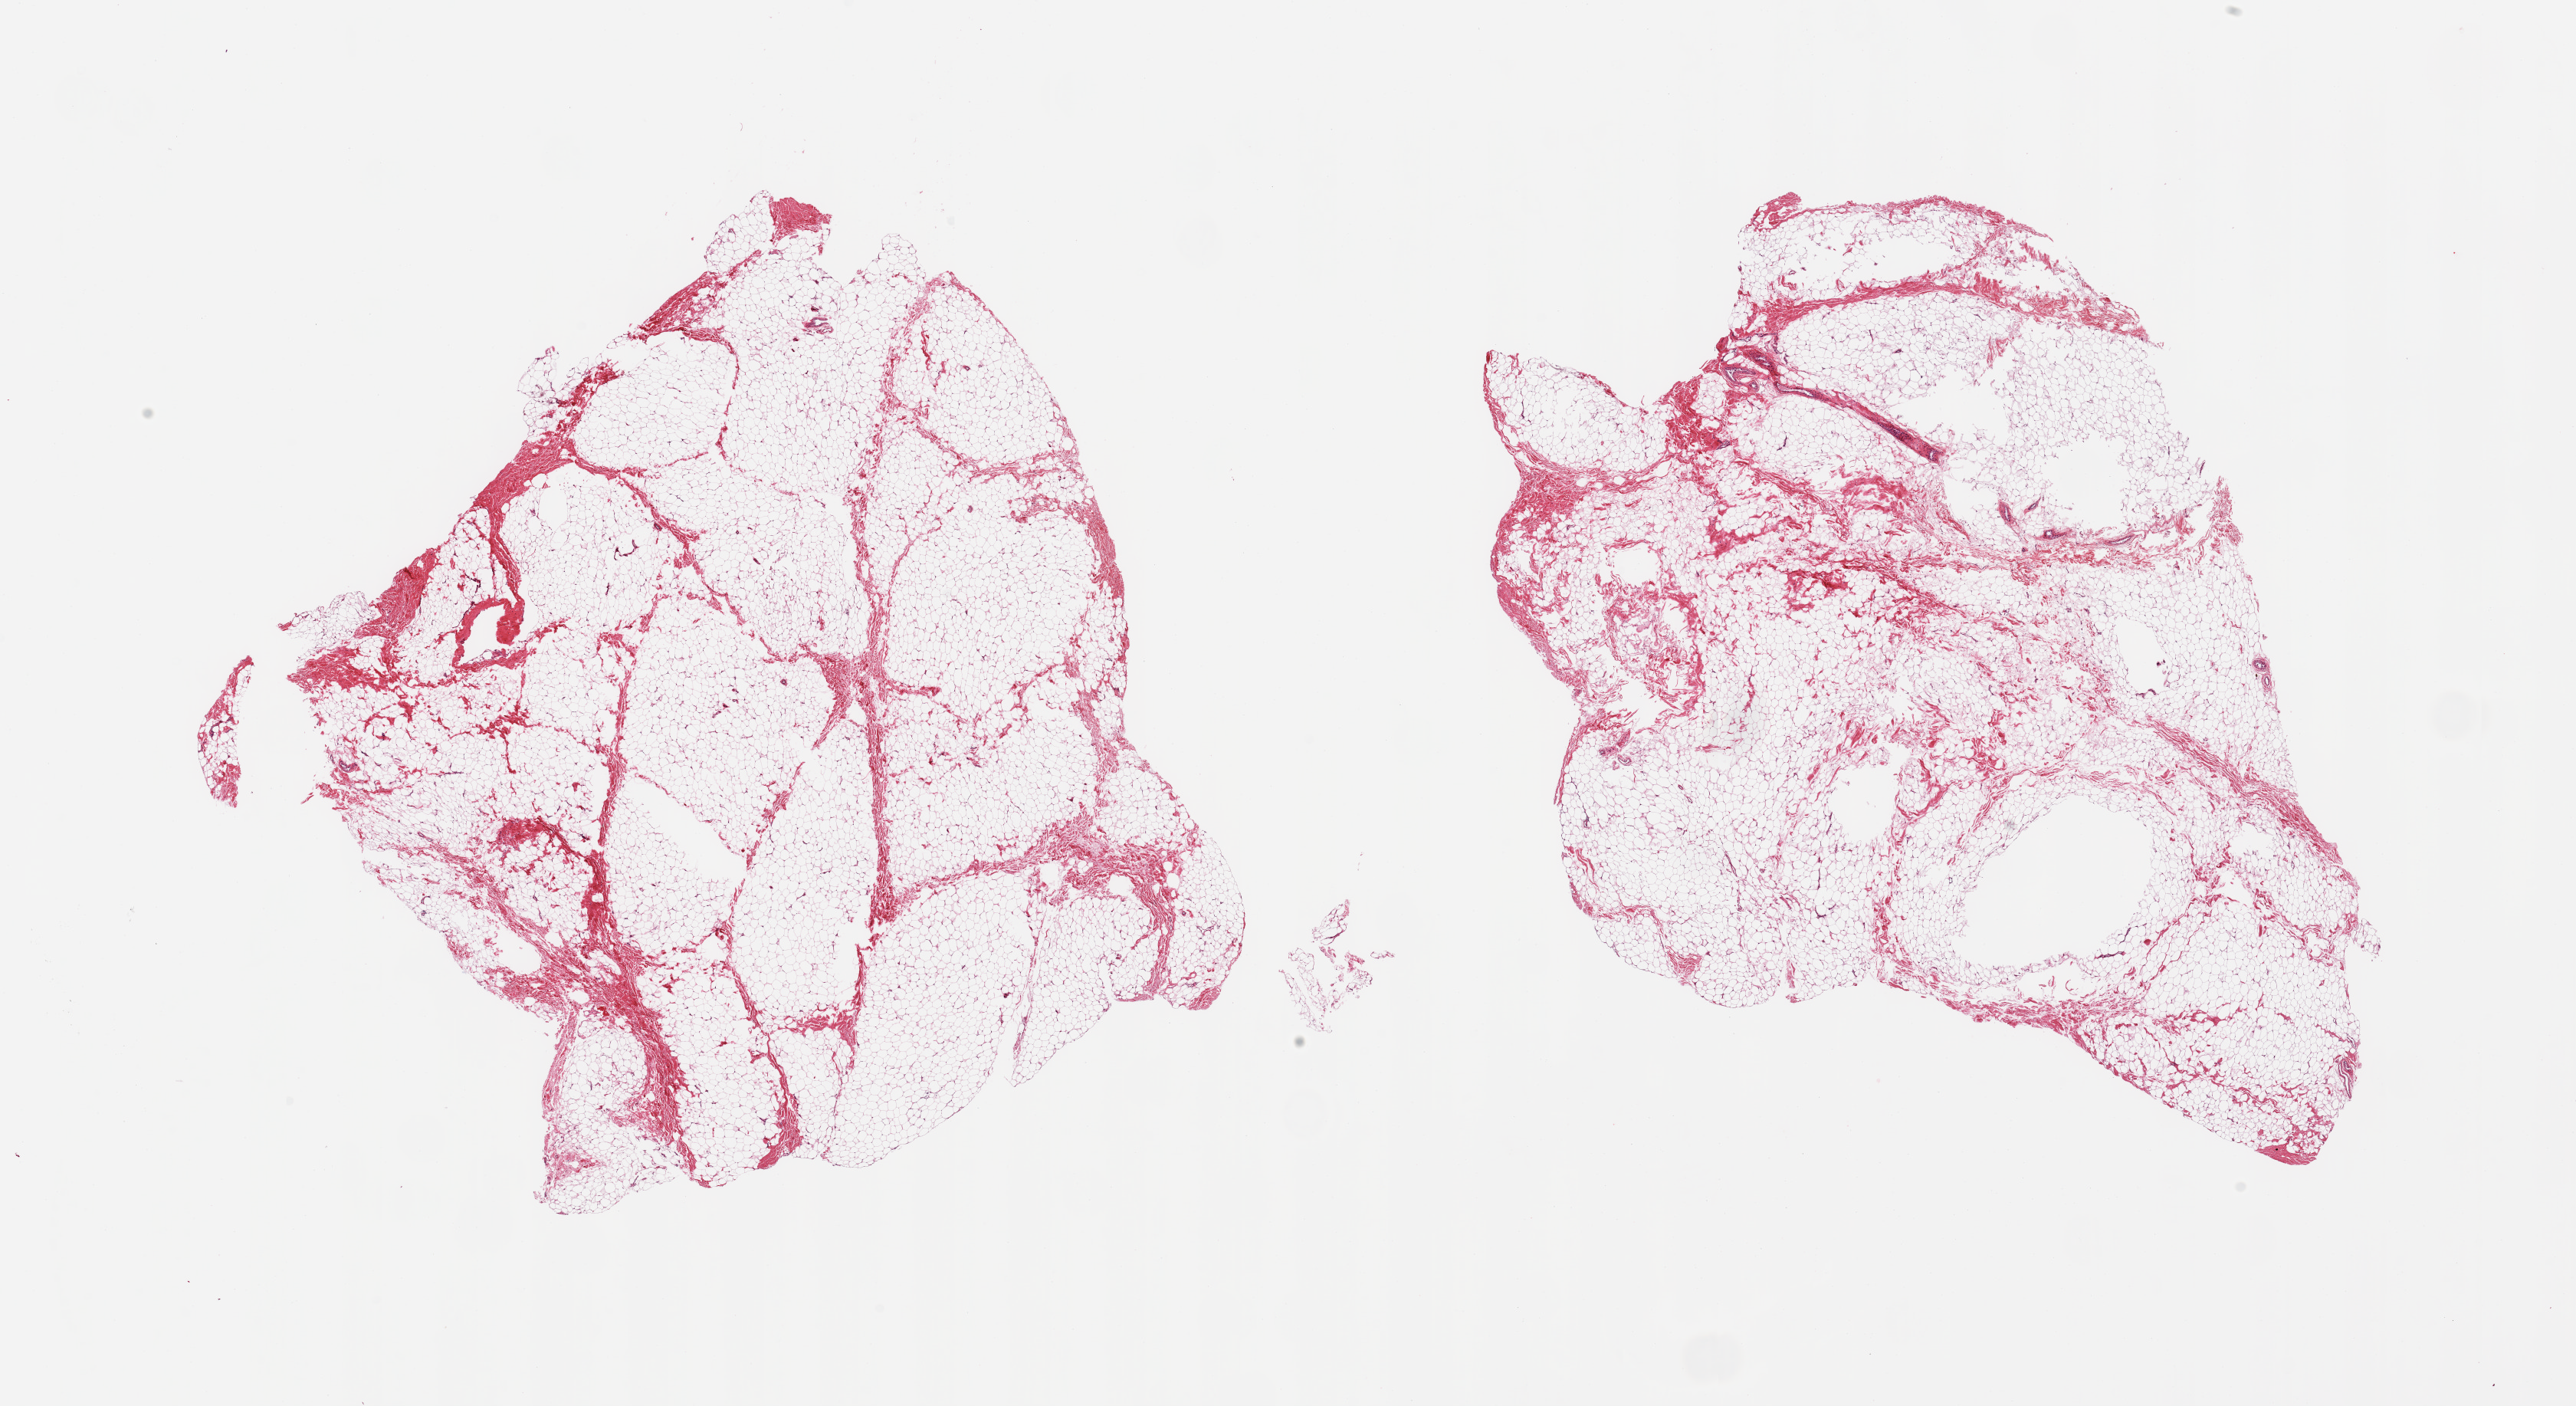
Whole-slide image, haematoxylin and eosin stain — shown as a low-resolution overview of the whole scanned area (about 26.6 x 14.5 mm), PAXgene-fixed, paraffin-embedded tissue, sampled site (target tissue): breast, tissue donor sample. Donor: male.
Reviewer comment on this tissue sample: 2 pieces; fibroadipose elements only.